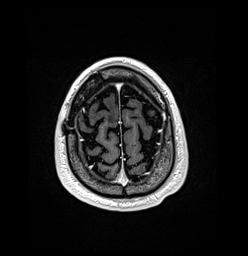
Brain MRI from a brain-tumour surgery series, one axial slice; slice 25 of 176 in the series (ordered by position); T1-weighted post-contrast; 248 × 256 image matrix, field of view 242 × 250 mm. From the clinical record (not read from this slice): histopathology: Oligodendroglioma; WHO grade: 3; IDH mutation: yes.
Structures marked on this image (outlined manually by an expert reader):
- previous resection cavity: bounding box (x1, y1, x2, y2) in pixels: (77, 115, 81, 119)